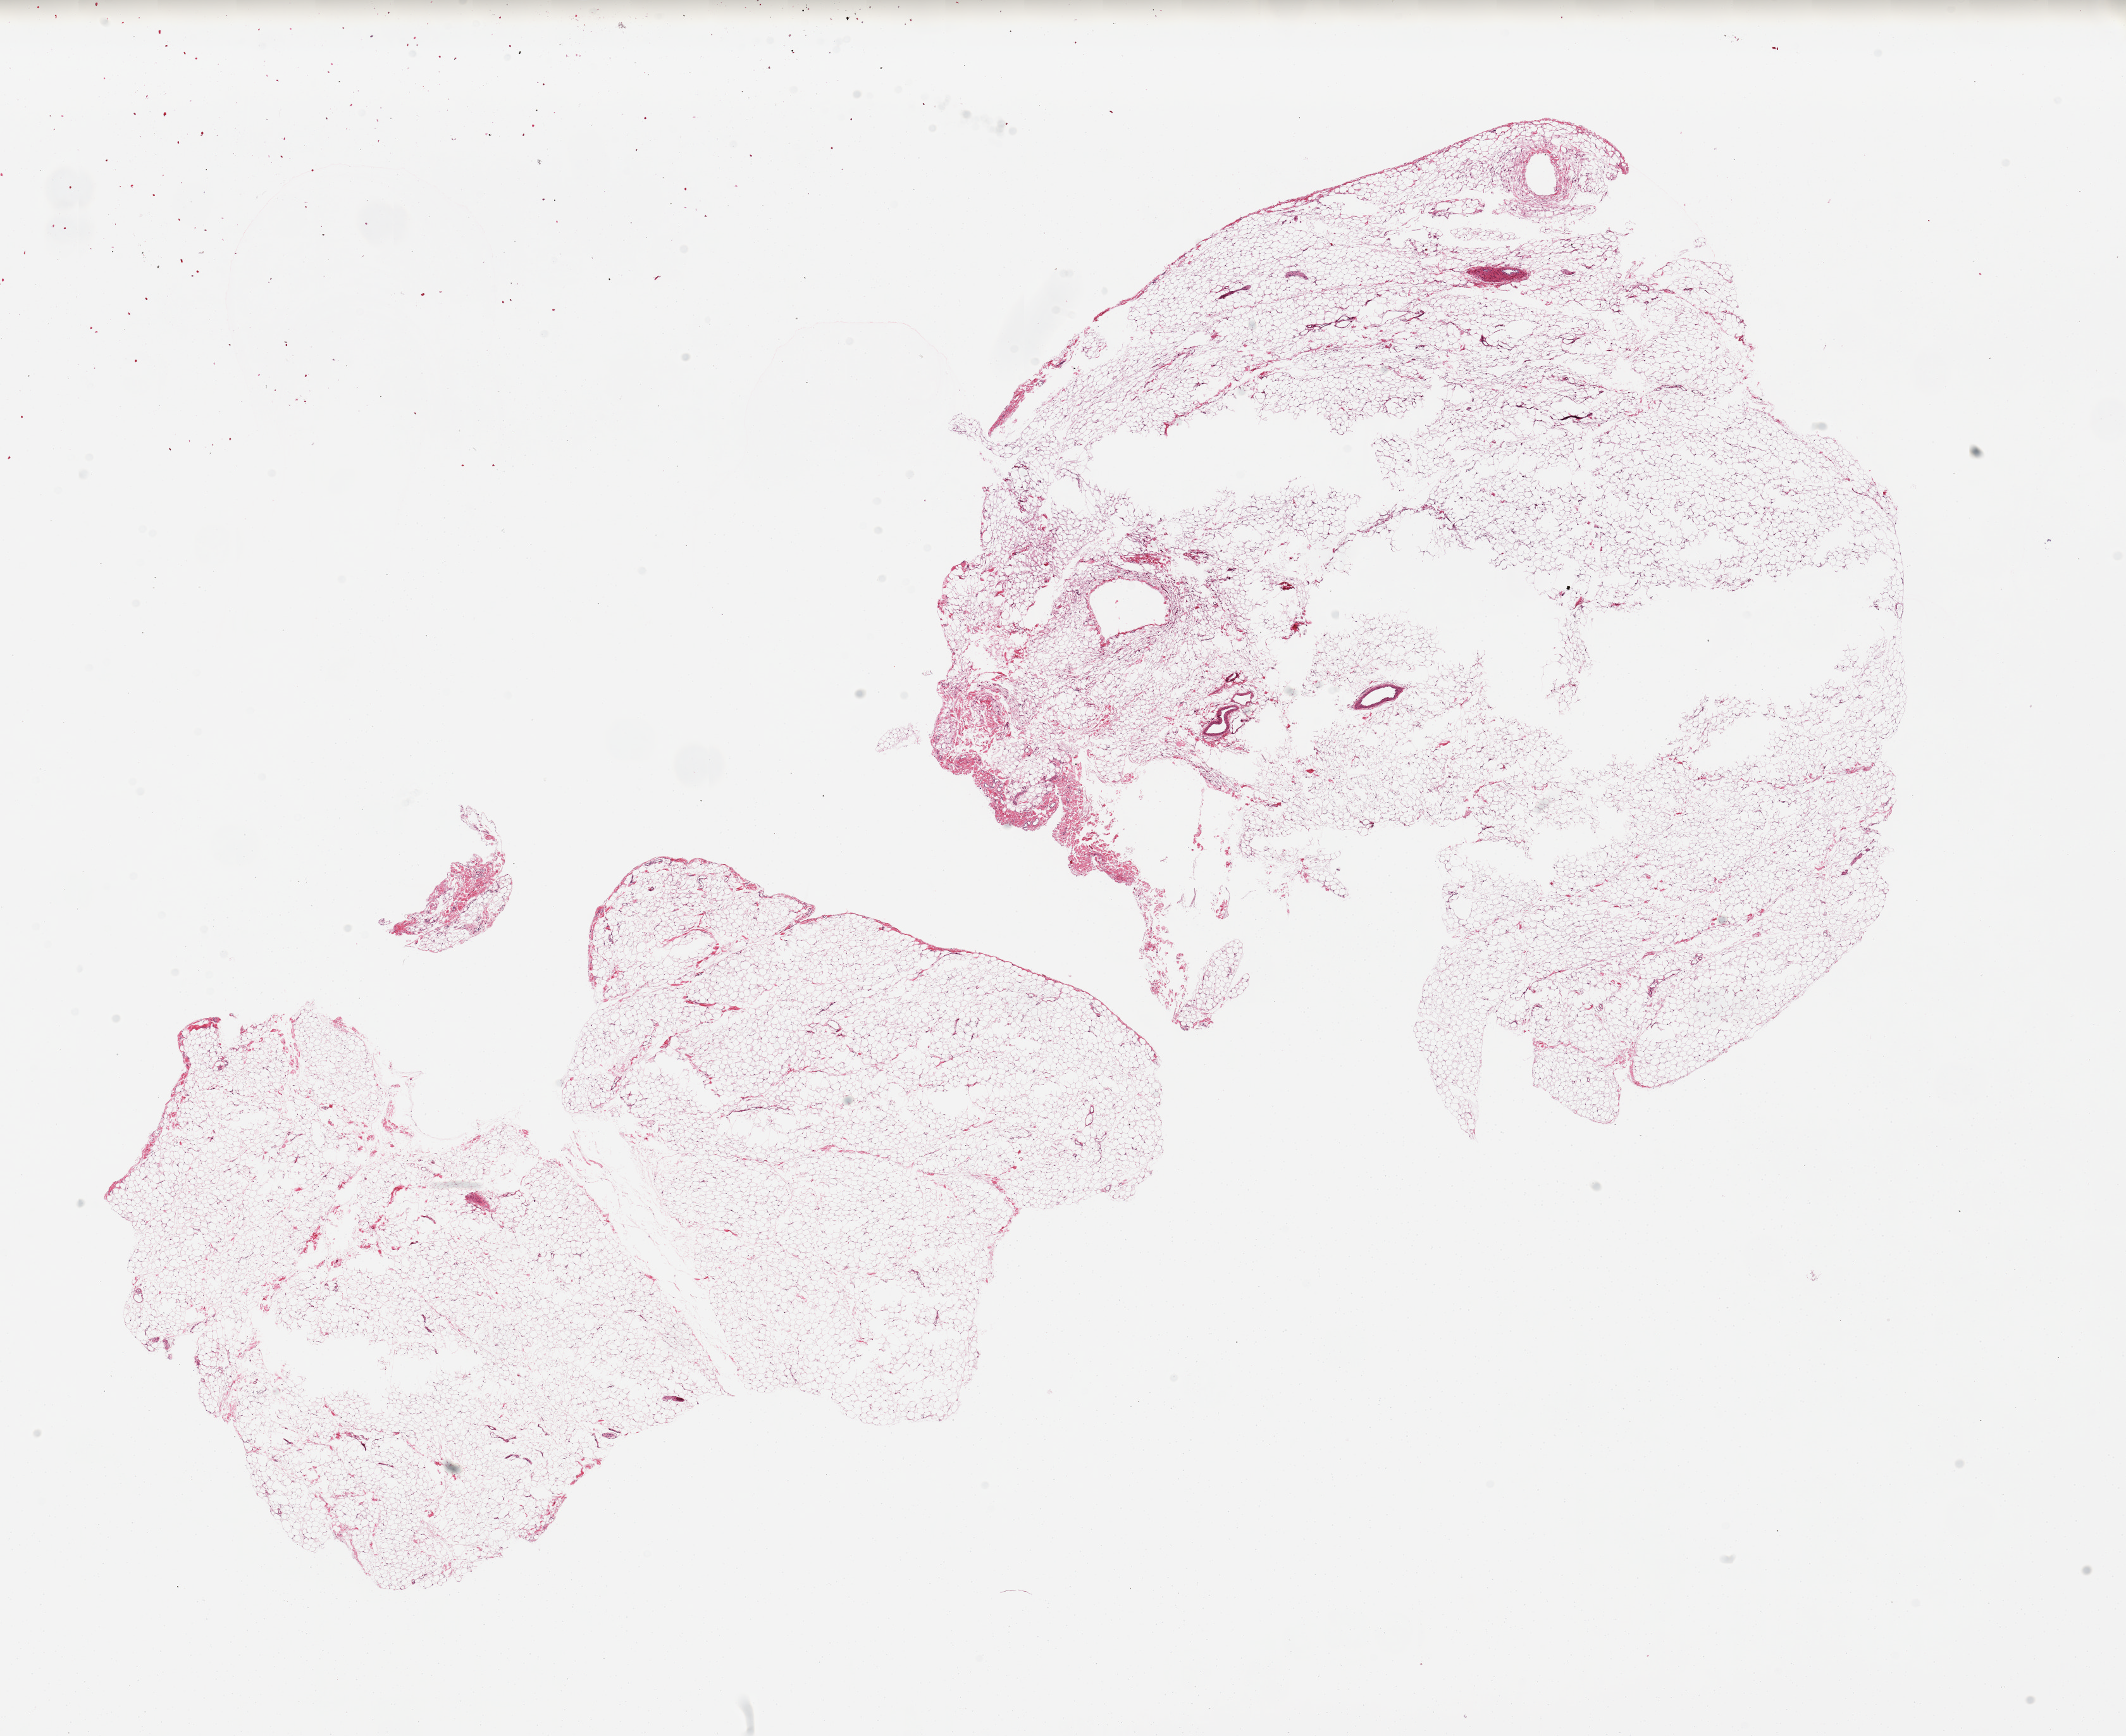
Digitized haematoxylin and eosin-stained section — shown as a low-resolution overview of the whole scanned area (about 26.6 x 21.7 mm), PAXgene-fixed, paraffin-embedded tissue, target tissue: omentum, donor tissue sample.
Reviewer comment on this tissue sample: 2 pieces; 1 is oversized and has central defects (? poor fixation).